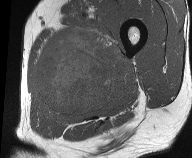
MRI of an extremity soft-tissue mass, one axial slice; position 23 of 61 along the scan axis; MR volume resampled by the dataset authors to the PET/CT grid (not the native acquisition matrix); 192 × 158 image matrix, field of view 187 × 154 mm. Male patient. Case-level facts recorded for this patient, not image findings: histological type: pleiomorphic liposarcoma; grade: high; site of the primary tumour: left thigh.
Annotated regions visible in this slice (expert contour drawn on MRI and transferred to this co-registered scan by the dataset authors):
- gross tumour volume including surrounding oedema: bounding box [x1, y1, x2, y2] px = [32, 27, 131, 120]
- gross tumour volume (mass): [36, 32, 113, 115]